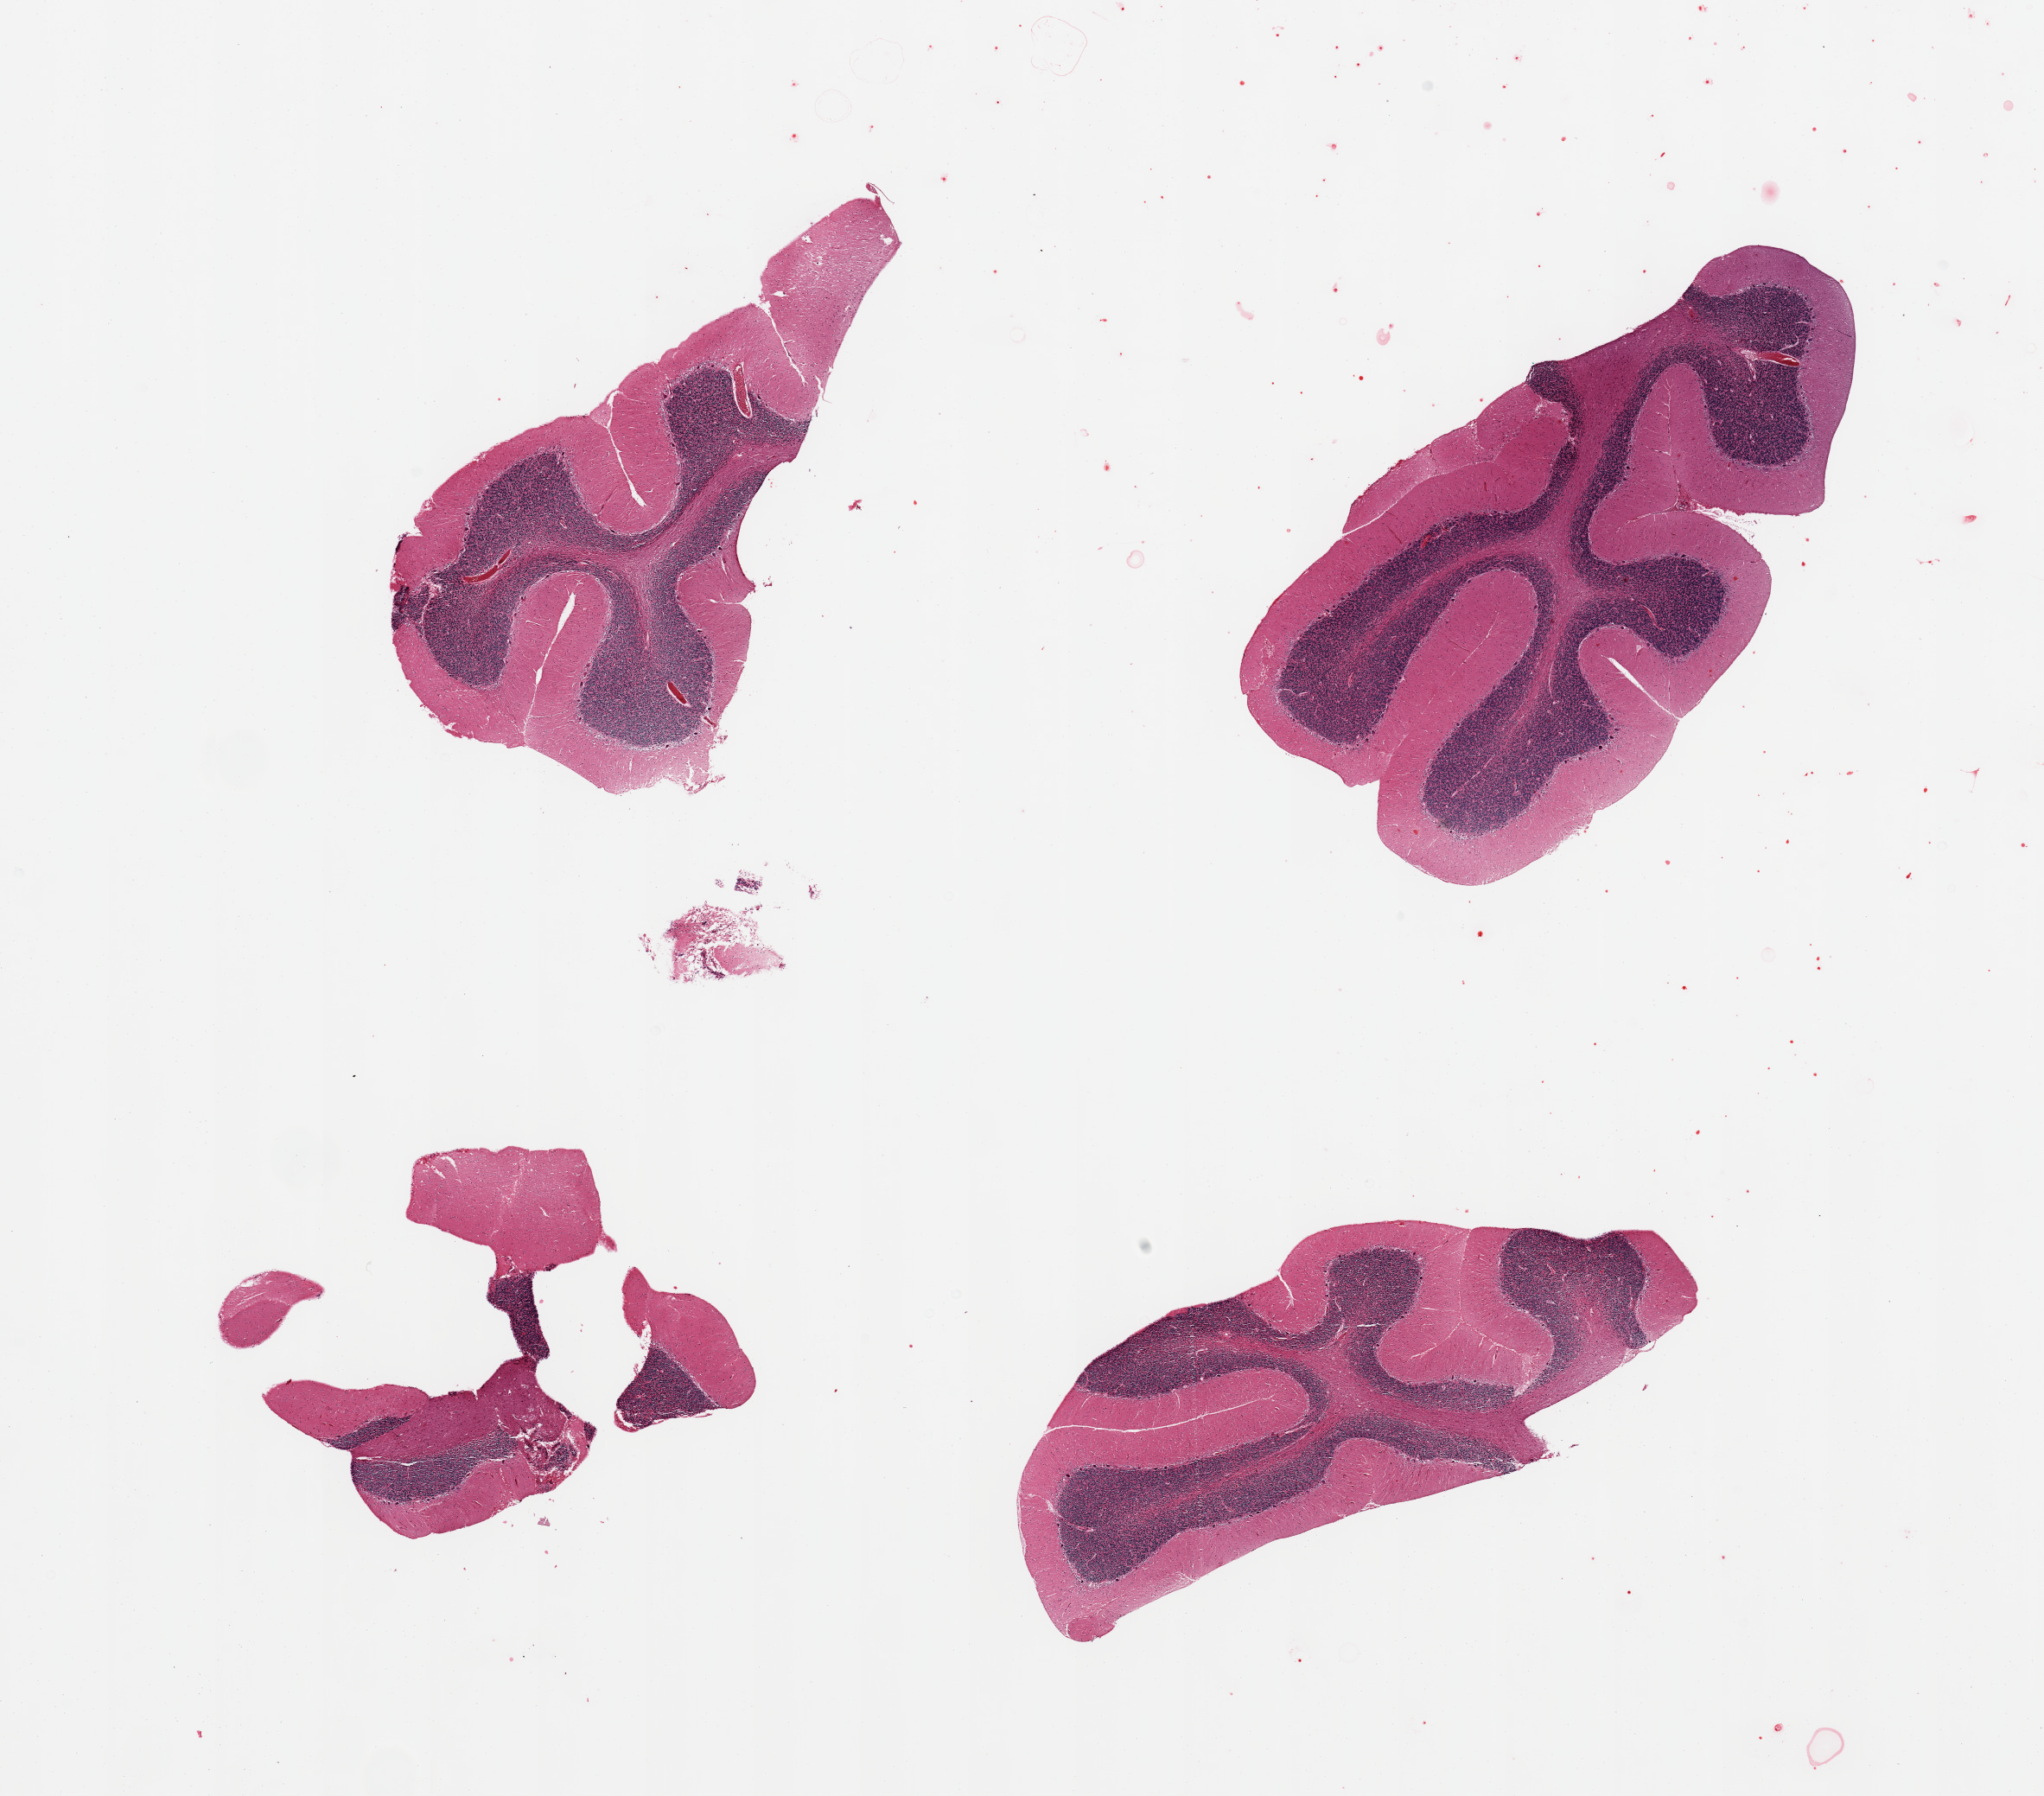
Whole-slide image, H&E stain, brightfield — a low-resolution overview of the entire scanned area, about 18.7 x 16.4 mm; PAXgene-fixed paraffin-embedded (PFPE) section; sampled site (target tissue): cerebellum; donor tissue sample. Male donor.
• pathologist's review note for this sample: 2 pieces, no abnormalities